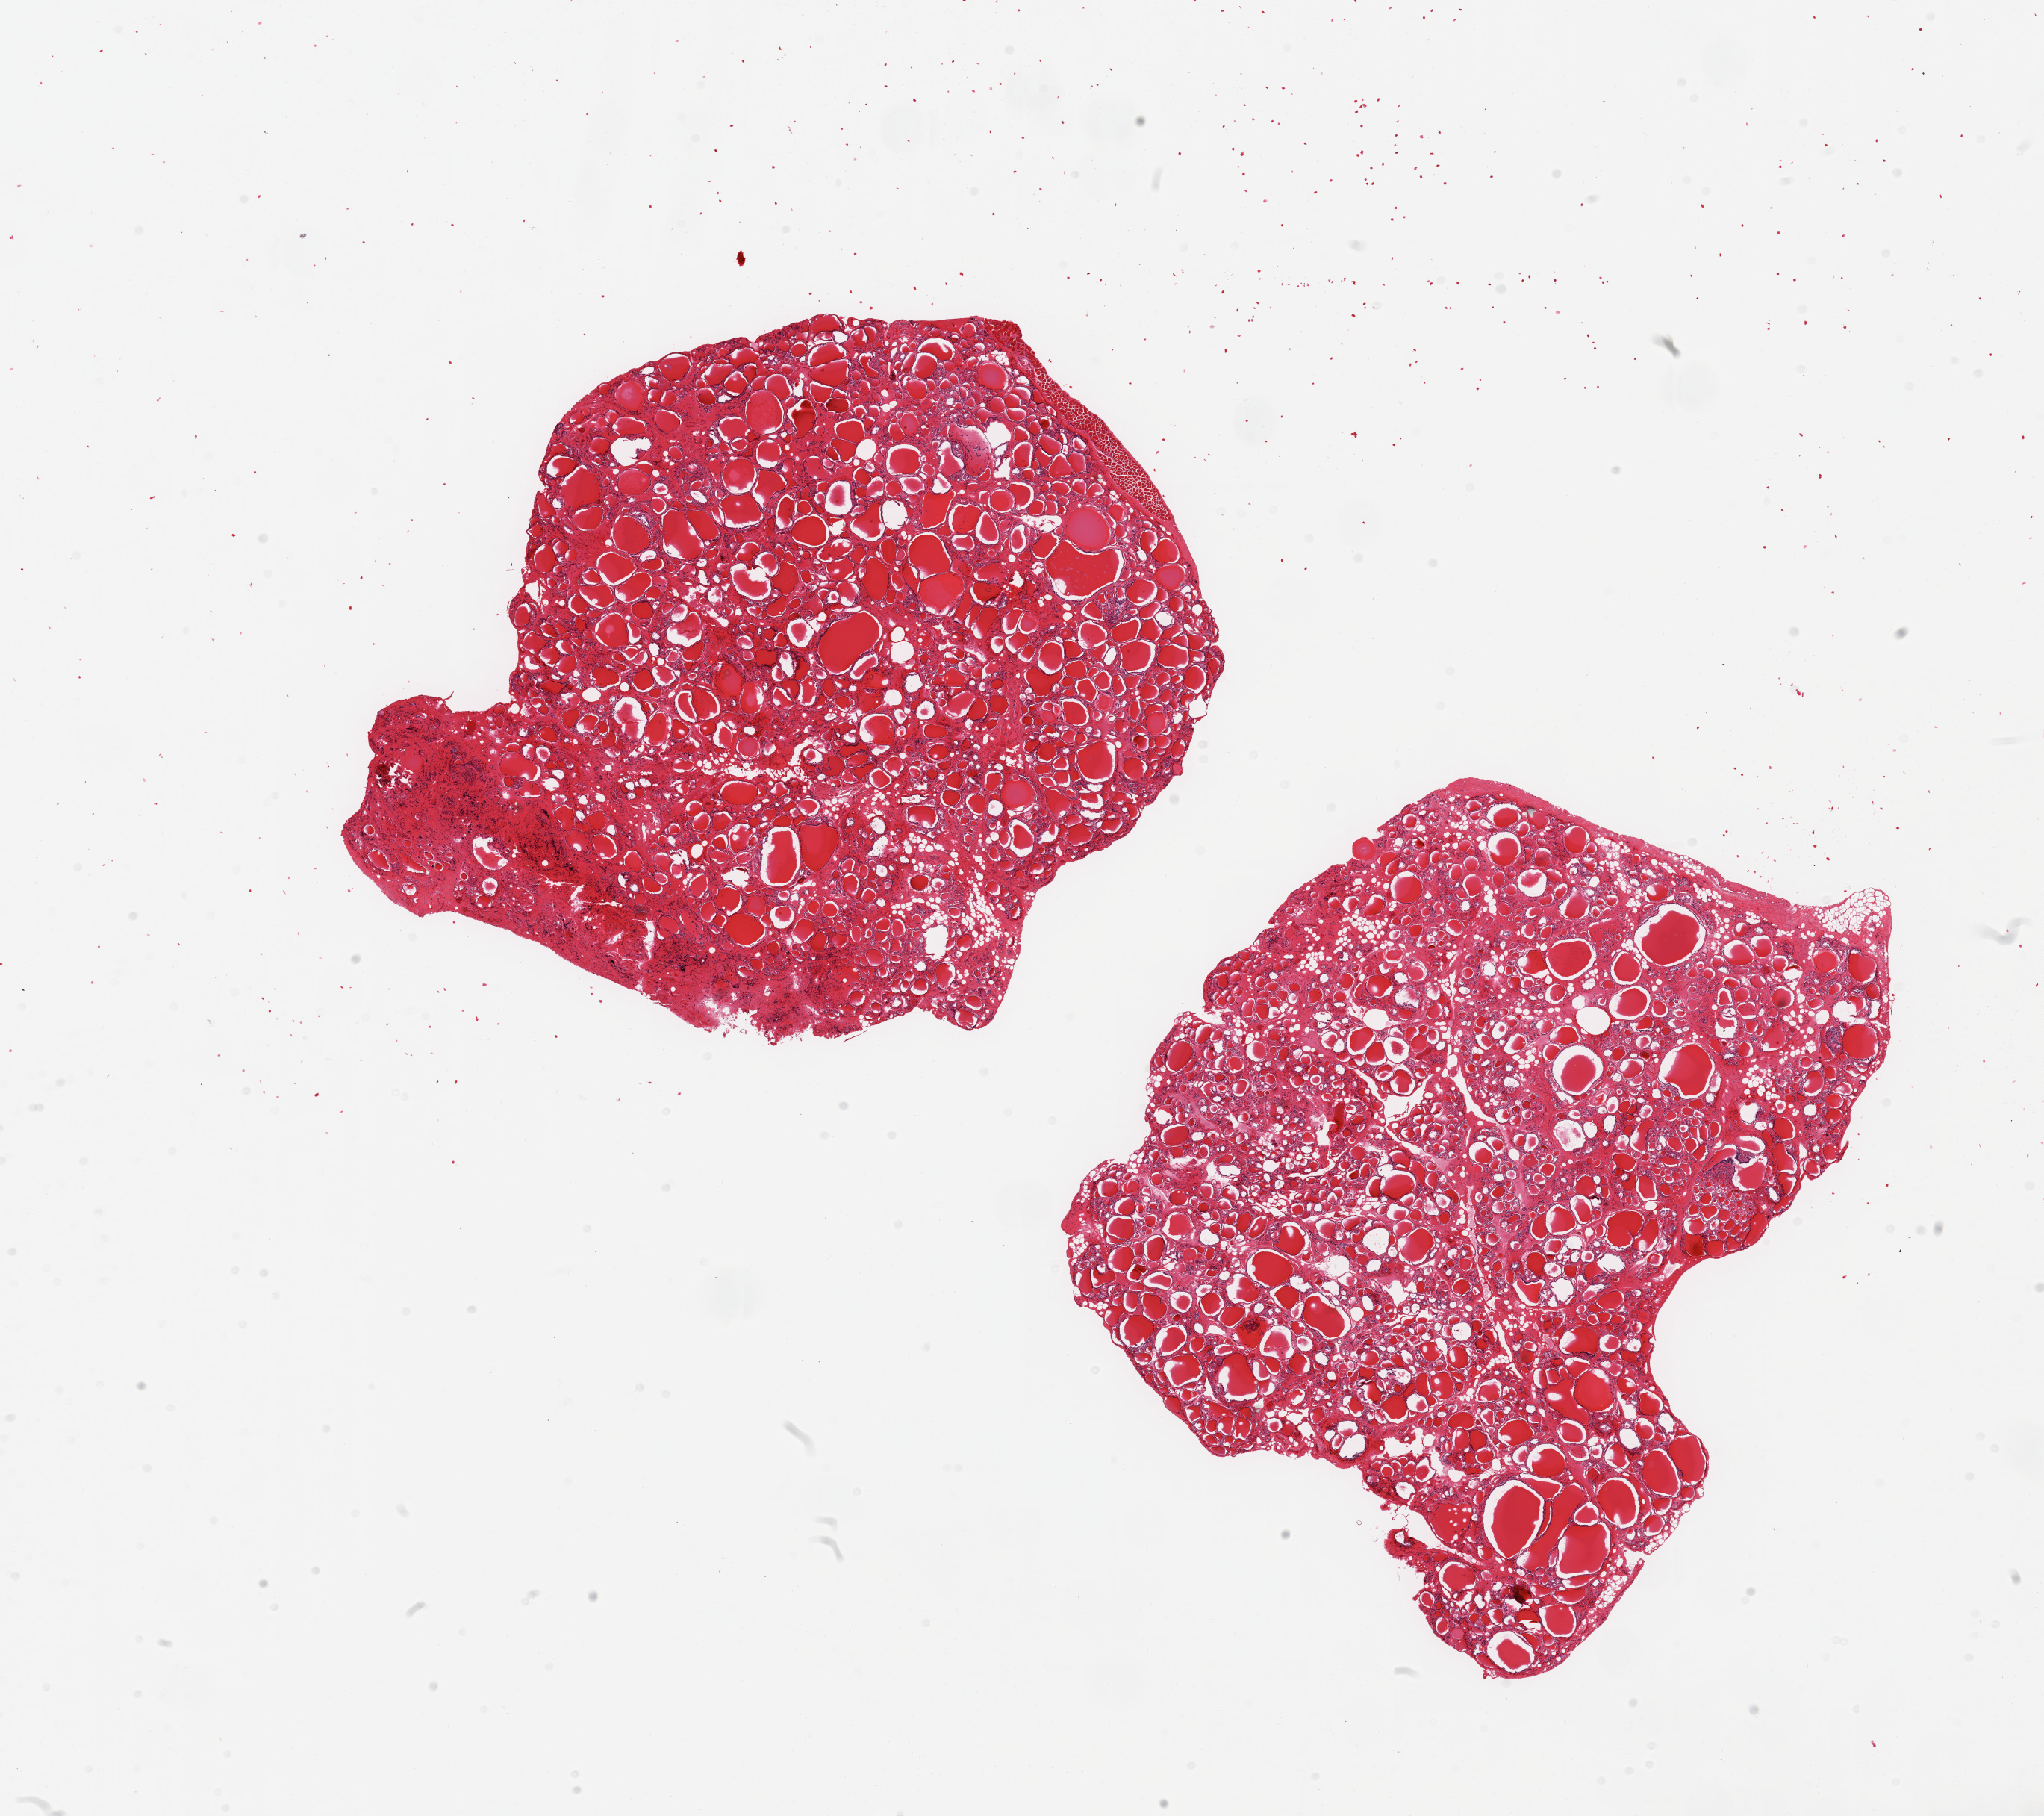
Whole-slide image, haematoxylin and eosin stain, shown as a low-resolution overview of the whole scanned area (about 21.7 x 19.2 mm, acquisition: 20x scan); PAXgene-fixed paraffin-embedded (PFPE) section; section of thyroid (target tissue); tissue donor sample. Donor sex: male.
- review note (as recorded): 2 pieces; attached thin rim of skeletal muscle; interstitial fibrosis